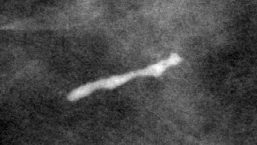
Cropped region of a digitized screen-film mammogram centred on a radiologist-marked abnormality, left breast, CC view.
Marked abnormality: calcifications, morphology large rodlike / round and regular, distribution regional; BI-RADS assessment category 2; subtlety rating 5 on a 1 (subtle) to 5 (obvious) scale; benign; no additional work-up was recommended (benign without callback).